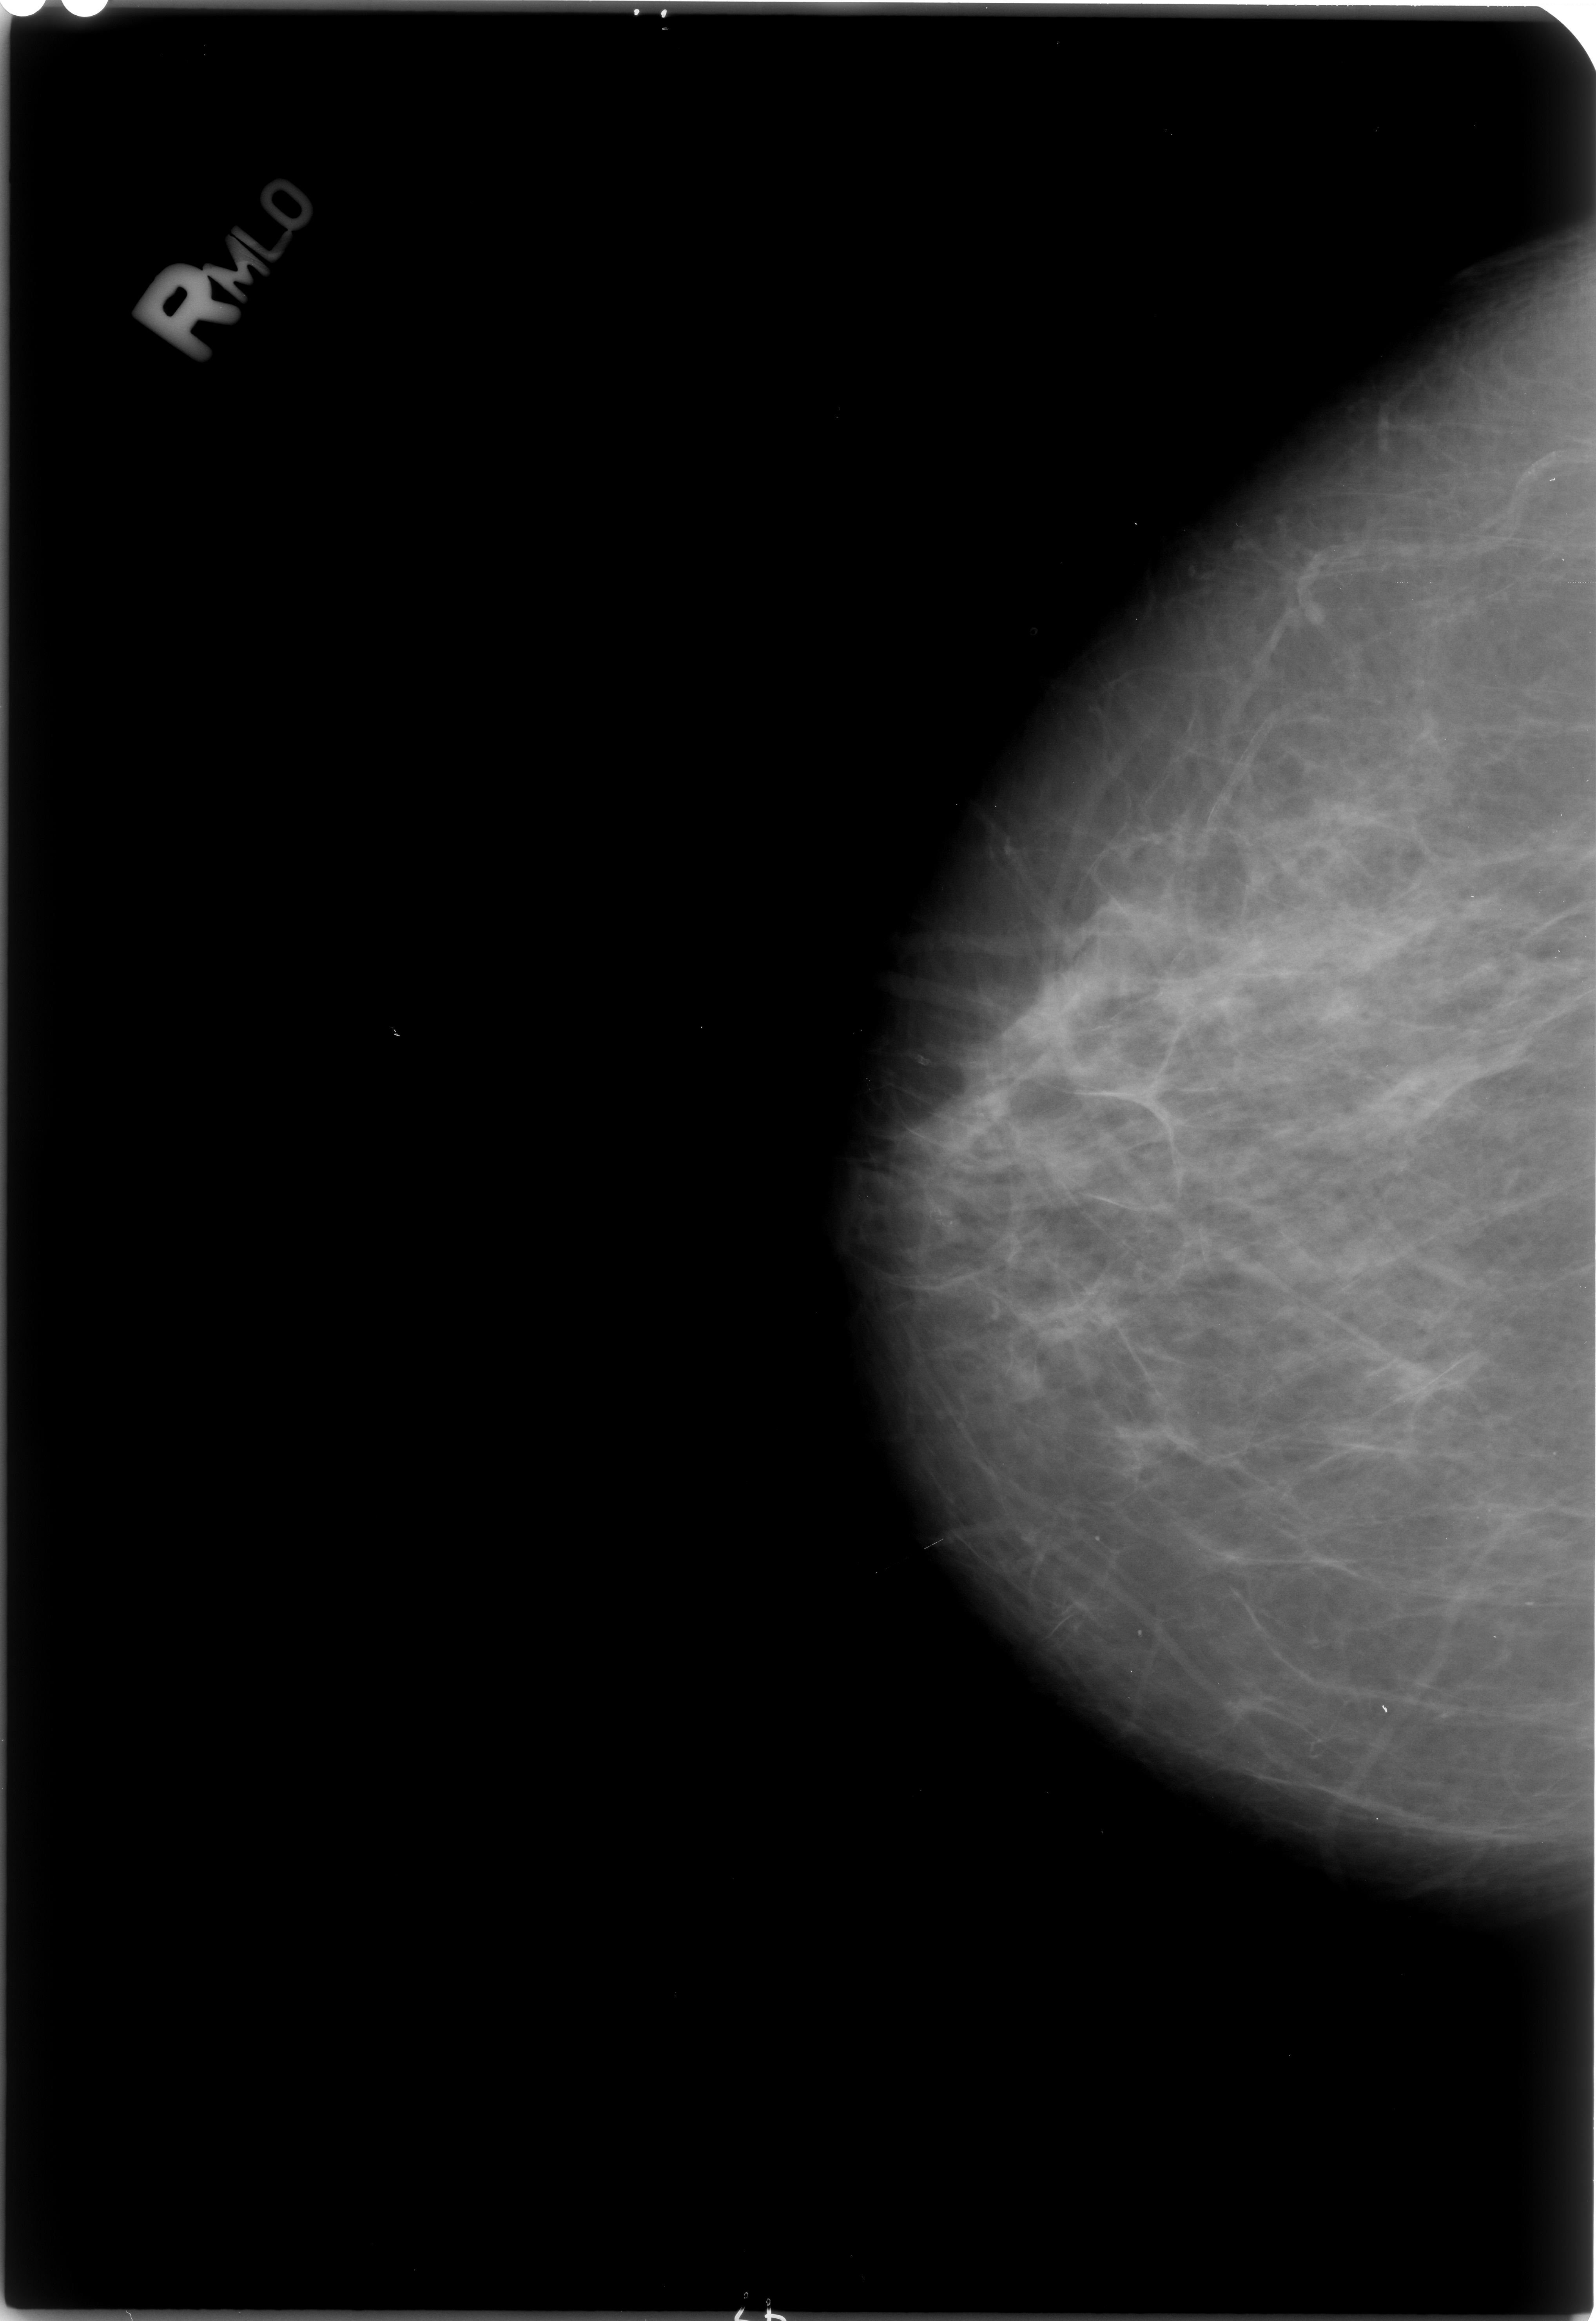
Mammogram (digitized film). Right breast. Craniocaudal (CC) view. BI-RADS breast density category 2 (scale 1–4). 1596 × 2321 image matrix.
Expert-marked regions of interest on this image (one box per marked abnormality):
- calcifications, morphology pleomorphic, distribution clustered; BI-RADS assessment category 4; pathology (as recorded): benign: bounding box [x1, y1, x2, y2] px = [903, 1185, 979, 1259]